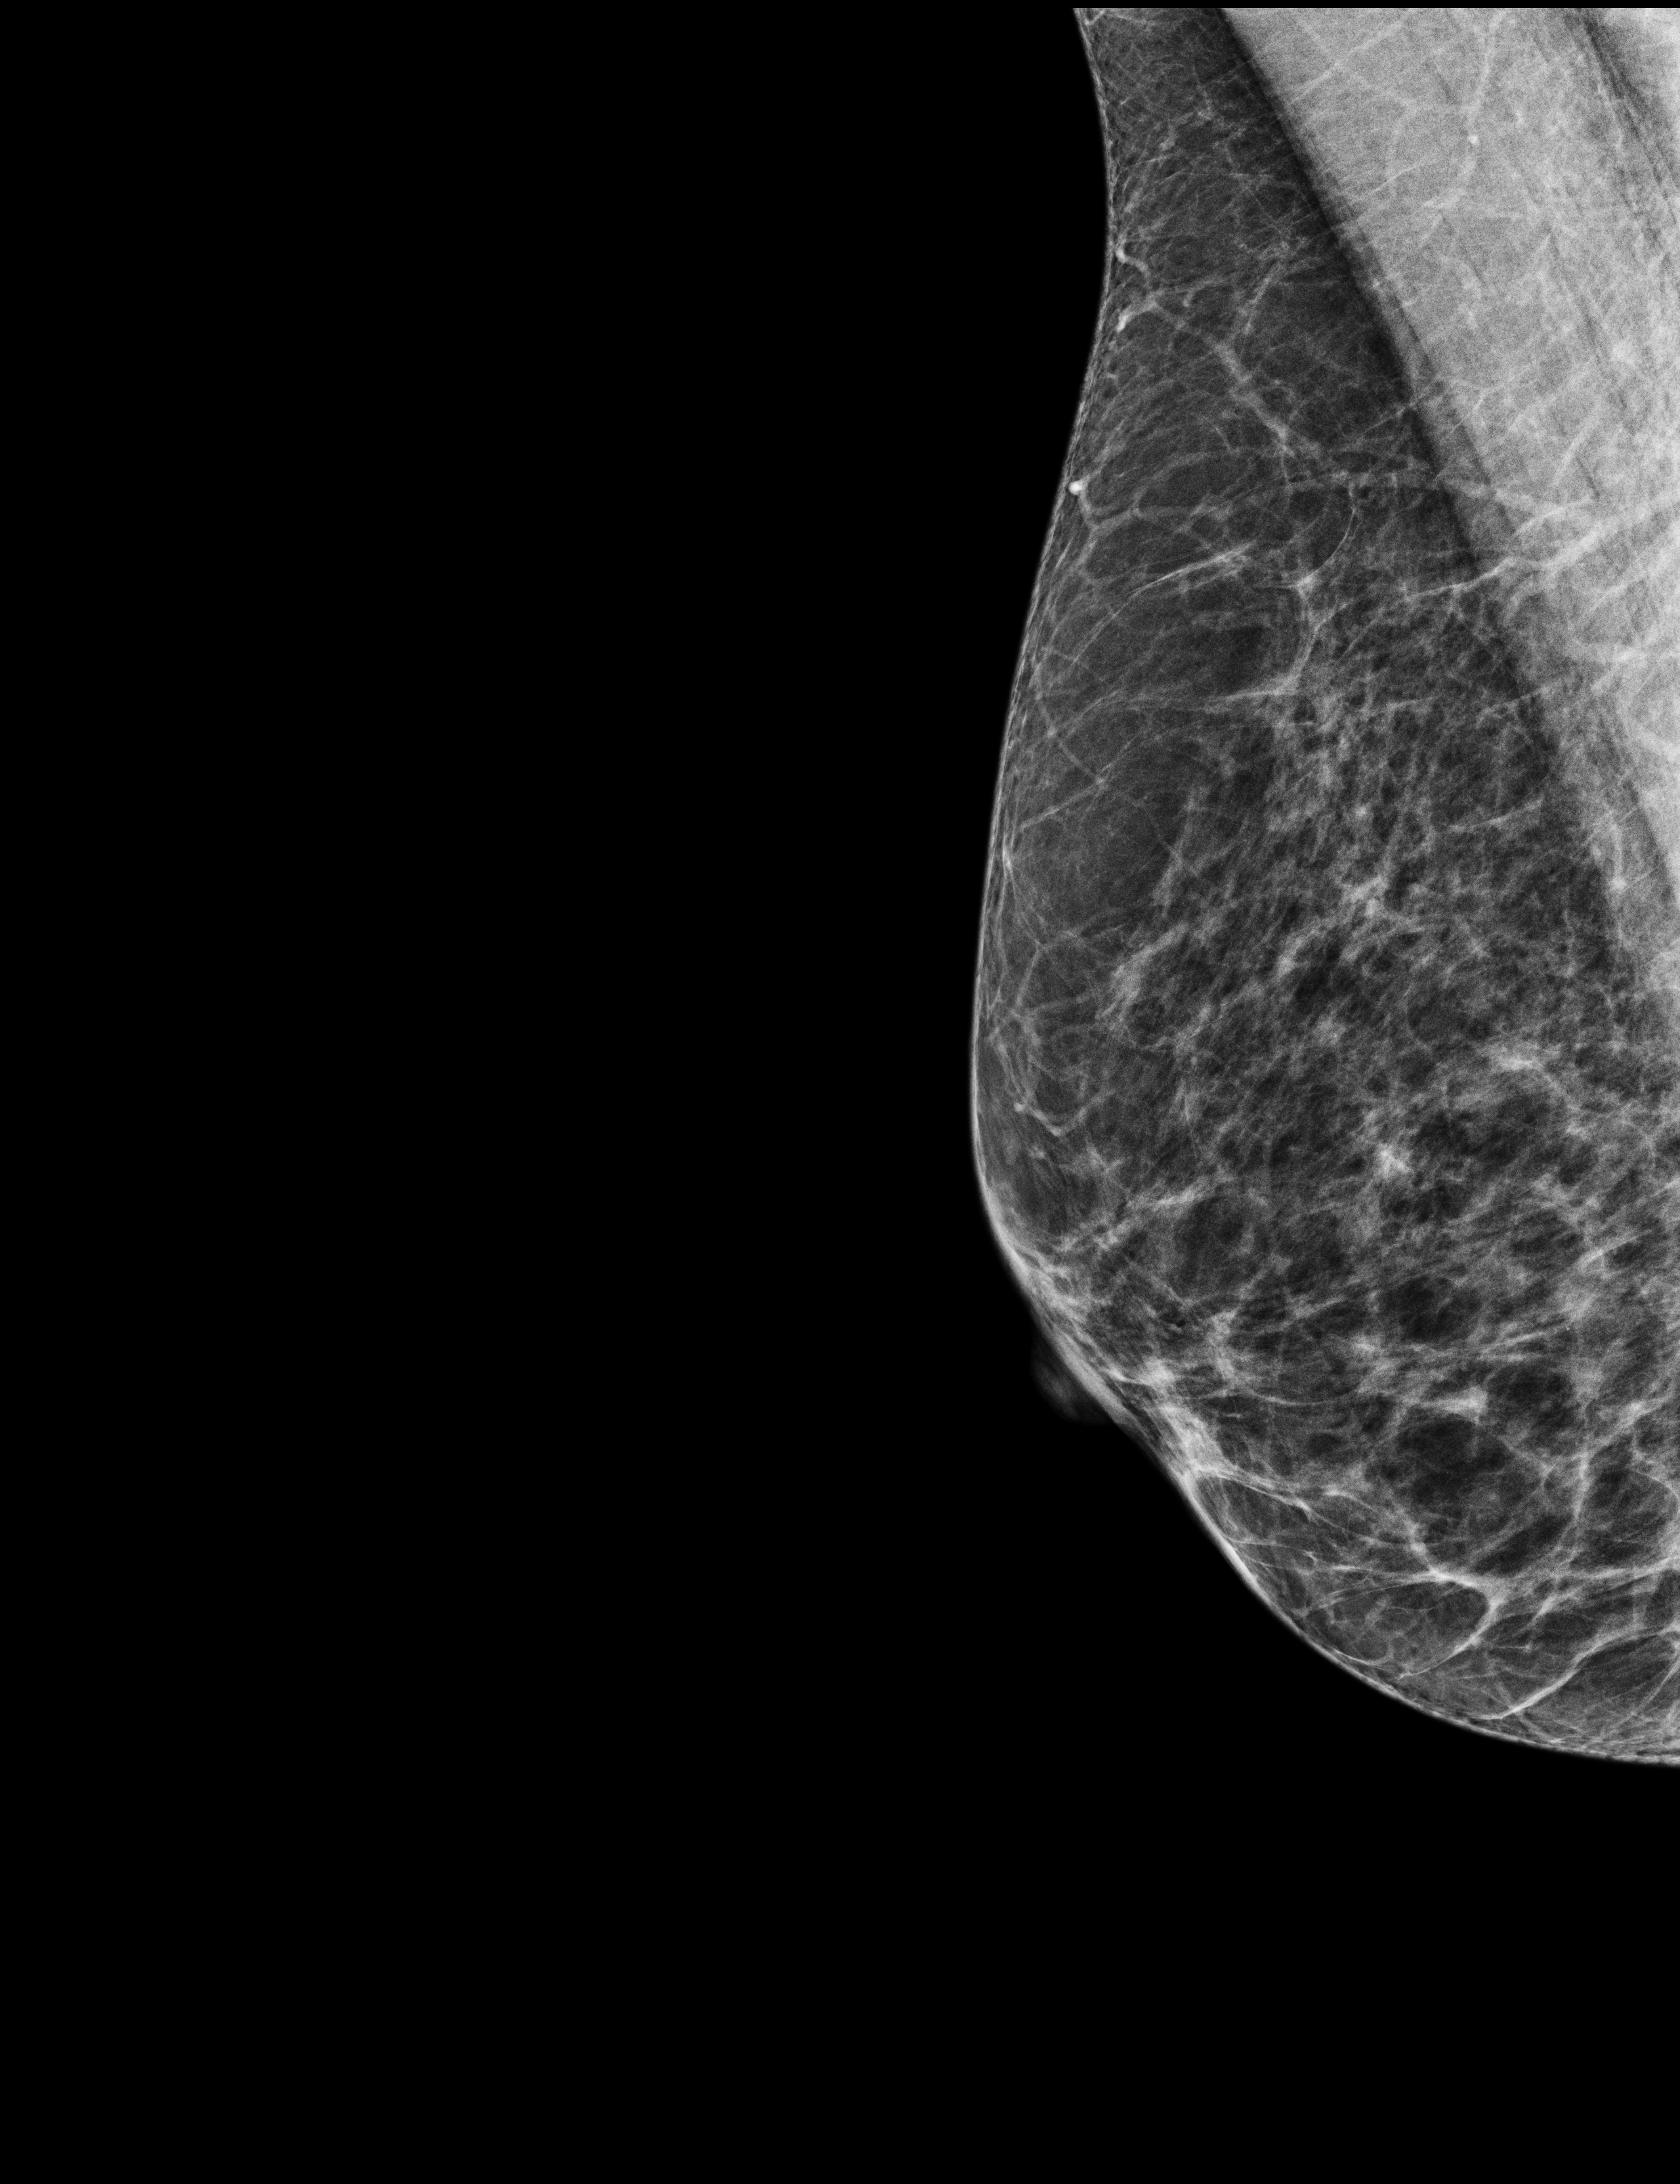
Screening examination; system: Selenia Dimensions. Patient aged 65 years (female).
Image type: full-field digital mammogram. Breast: right. Projection: MLO view.